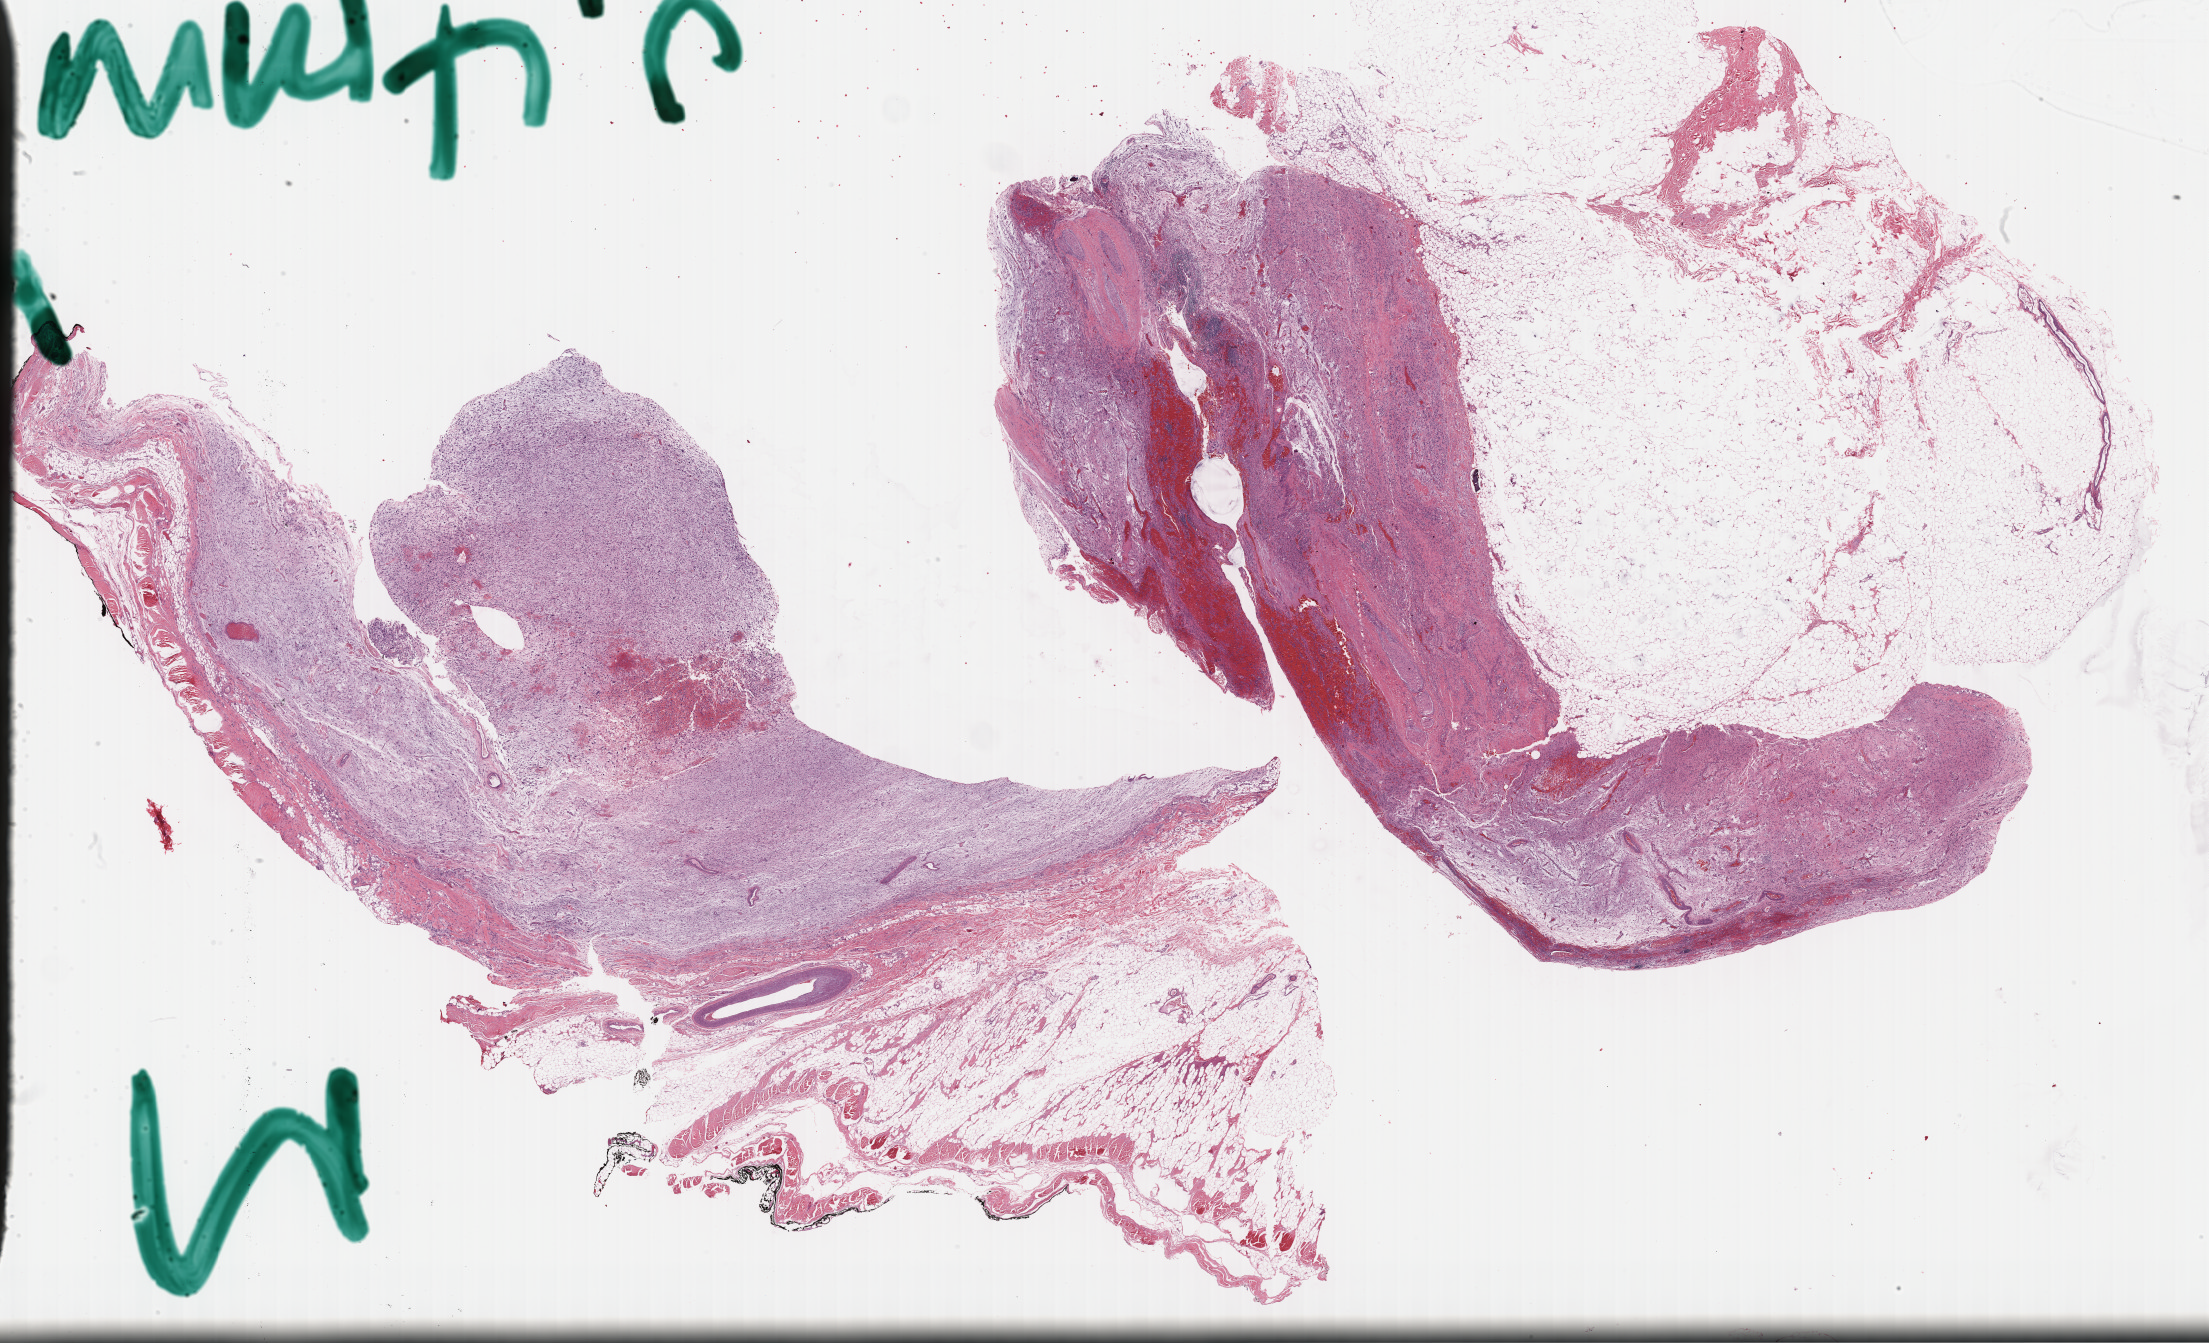
Digitized H&E tissue section (whole slide) — shown as a low-resolution overview of the whole scanned area (about 35.7 x 21.7 mm, slide scanned at 40x); formalin-fixed paraffin-embedded (FFPE) diagnostic section; connective, subcutaneous and other soft tissues, primary tumour sample. Patient sex: male.
Diagnosis: Fibromyxosarcoma (connective, subcutaneous and other soft tissues of trunk, NOS).